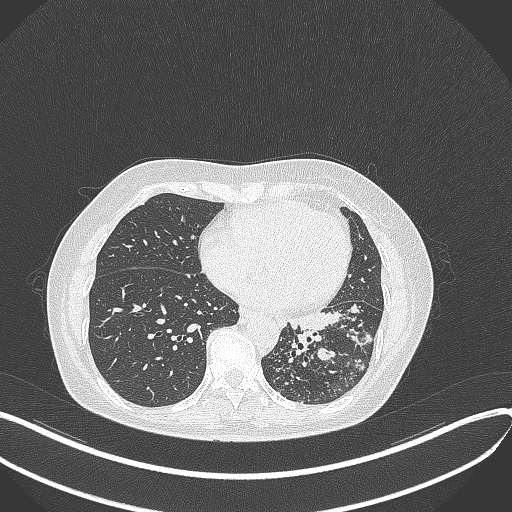
Chest CT, one axial slice; slice 150 of 429 in the series (ordered by position); reconstruction kernel B70f; 100 kVp; lung window (W 1500 / L -600 HU); 1 mm slice thickness; 512 × 512 image matrix. Female patient, age 63 years. From the clinical record (not read from this slice): clinical TNM (as recorded): T1b N0 M0; histopathological grade: G2-3.
Outlined on this slice (bounding box drawn by a radiologist):
- lung tumour (recorded histology: adenocarcinoma): box from (x=284, y=304) to (x=375, y=345) px